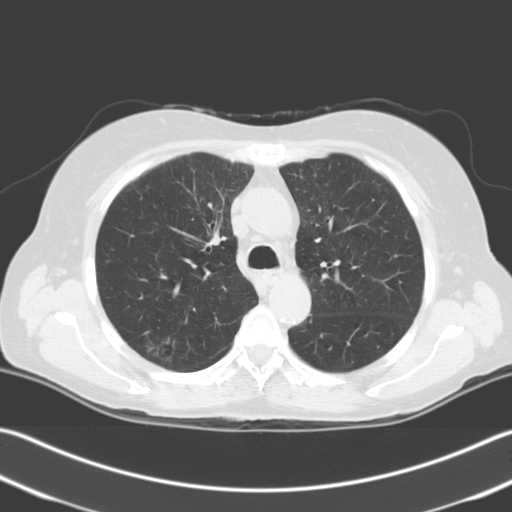
Axial slice from a low-dose chest CT screening exam; baseline annual screen; lung window (W 1500 / L -600 HU); 3.2 mm slice thickness; standard (soft-tissue) reconstruction kernel (C). Female participant, aged 67 years at enrolment. Current smoker at enrolment.
Expert-annotated lung lesion, bounding box (x1, y1, x2, y2) in pixels: (124, 325, 183, 373). The screening reader recorded 2 non-calcified nodules or masses ≥4 mm on this exam (right upper lobe, right upper lobe); which of them this box marks is not recorded. Participant outcome: lung cancer diagnosed 24 days after this screen — squamous cell carcinoma, NOS, right upper lobe, stage IIIA (AJCC 6th edition), 56 mm at pathology.